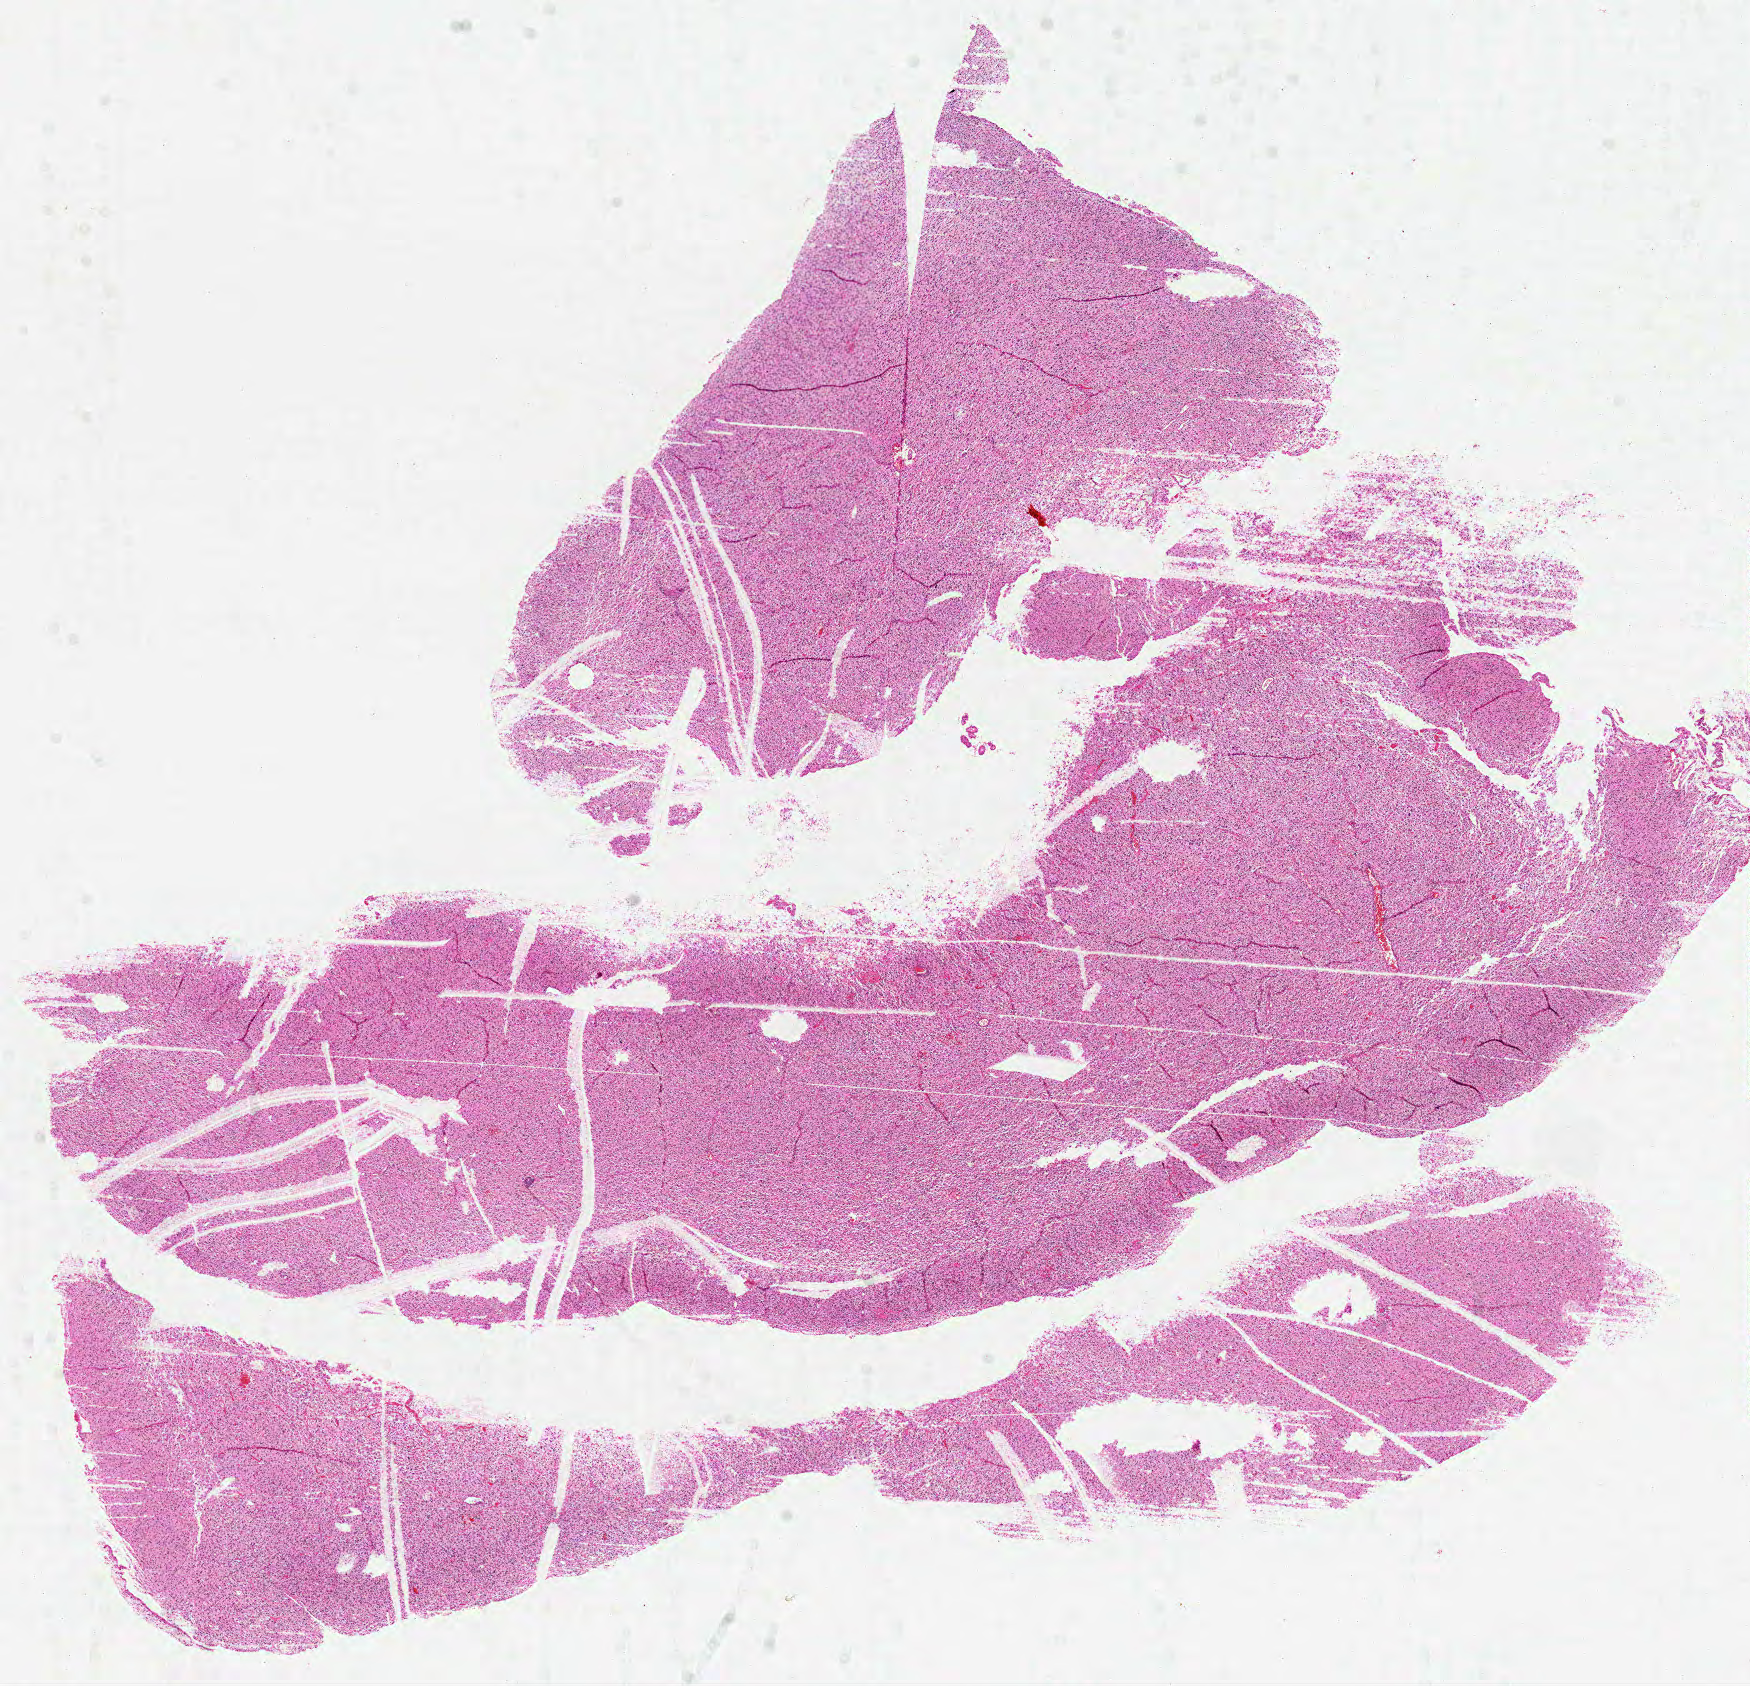
Digitized H&E tissue section (whole slide) — a low-resolution overview of the entire scanned area, about 14.0 x 13.5 mm; formalin-fixed paraffin-embedded (FFPE) diagnostic section; brain, primary tumour sample. Patient: female, age at initial diagnosis 36 years.
Histologic diagnosis: Glioblastoma.